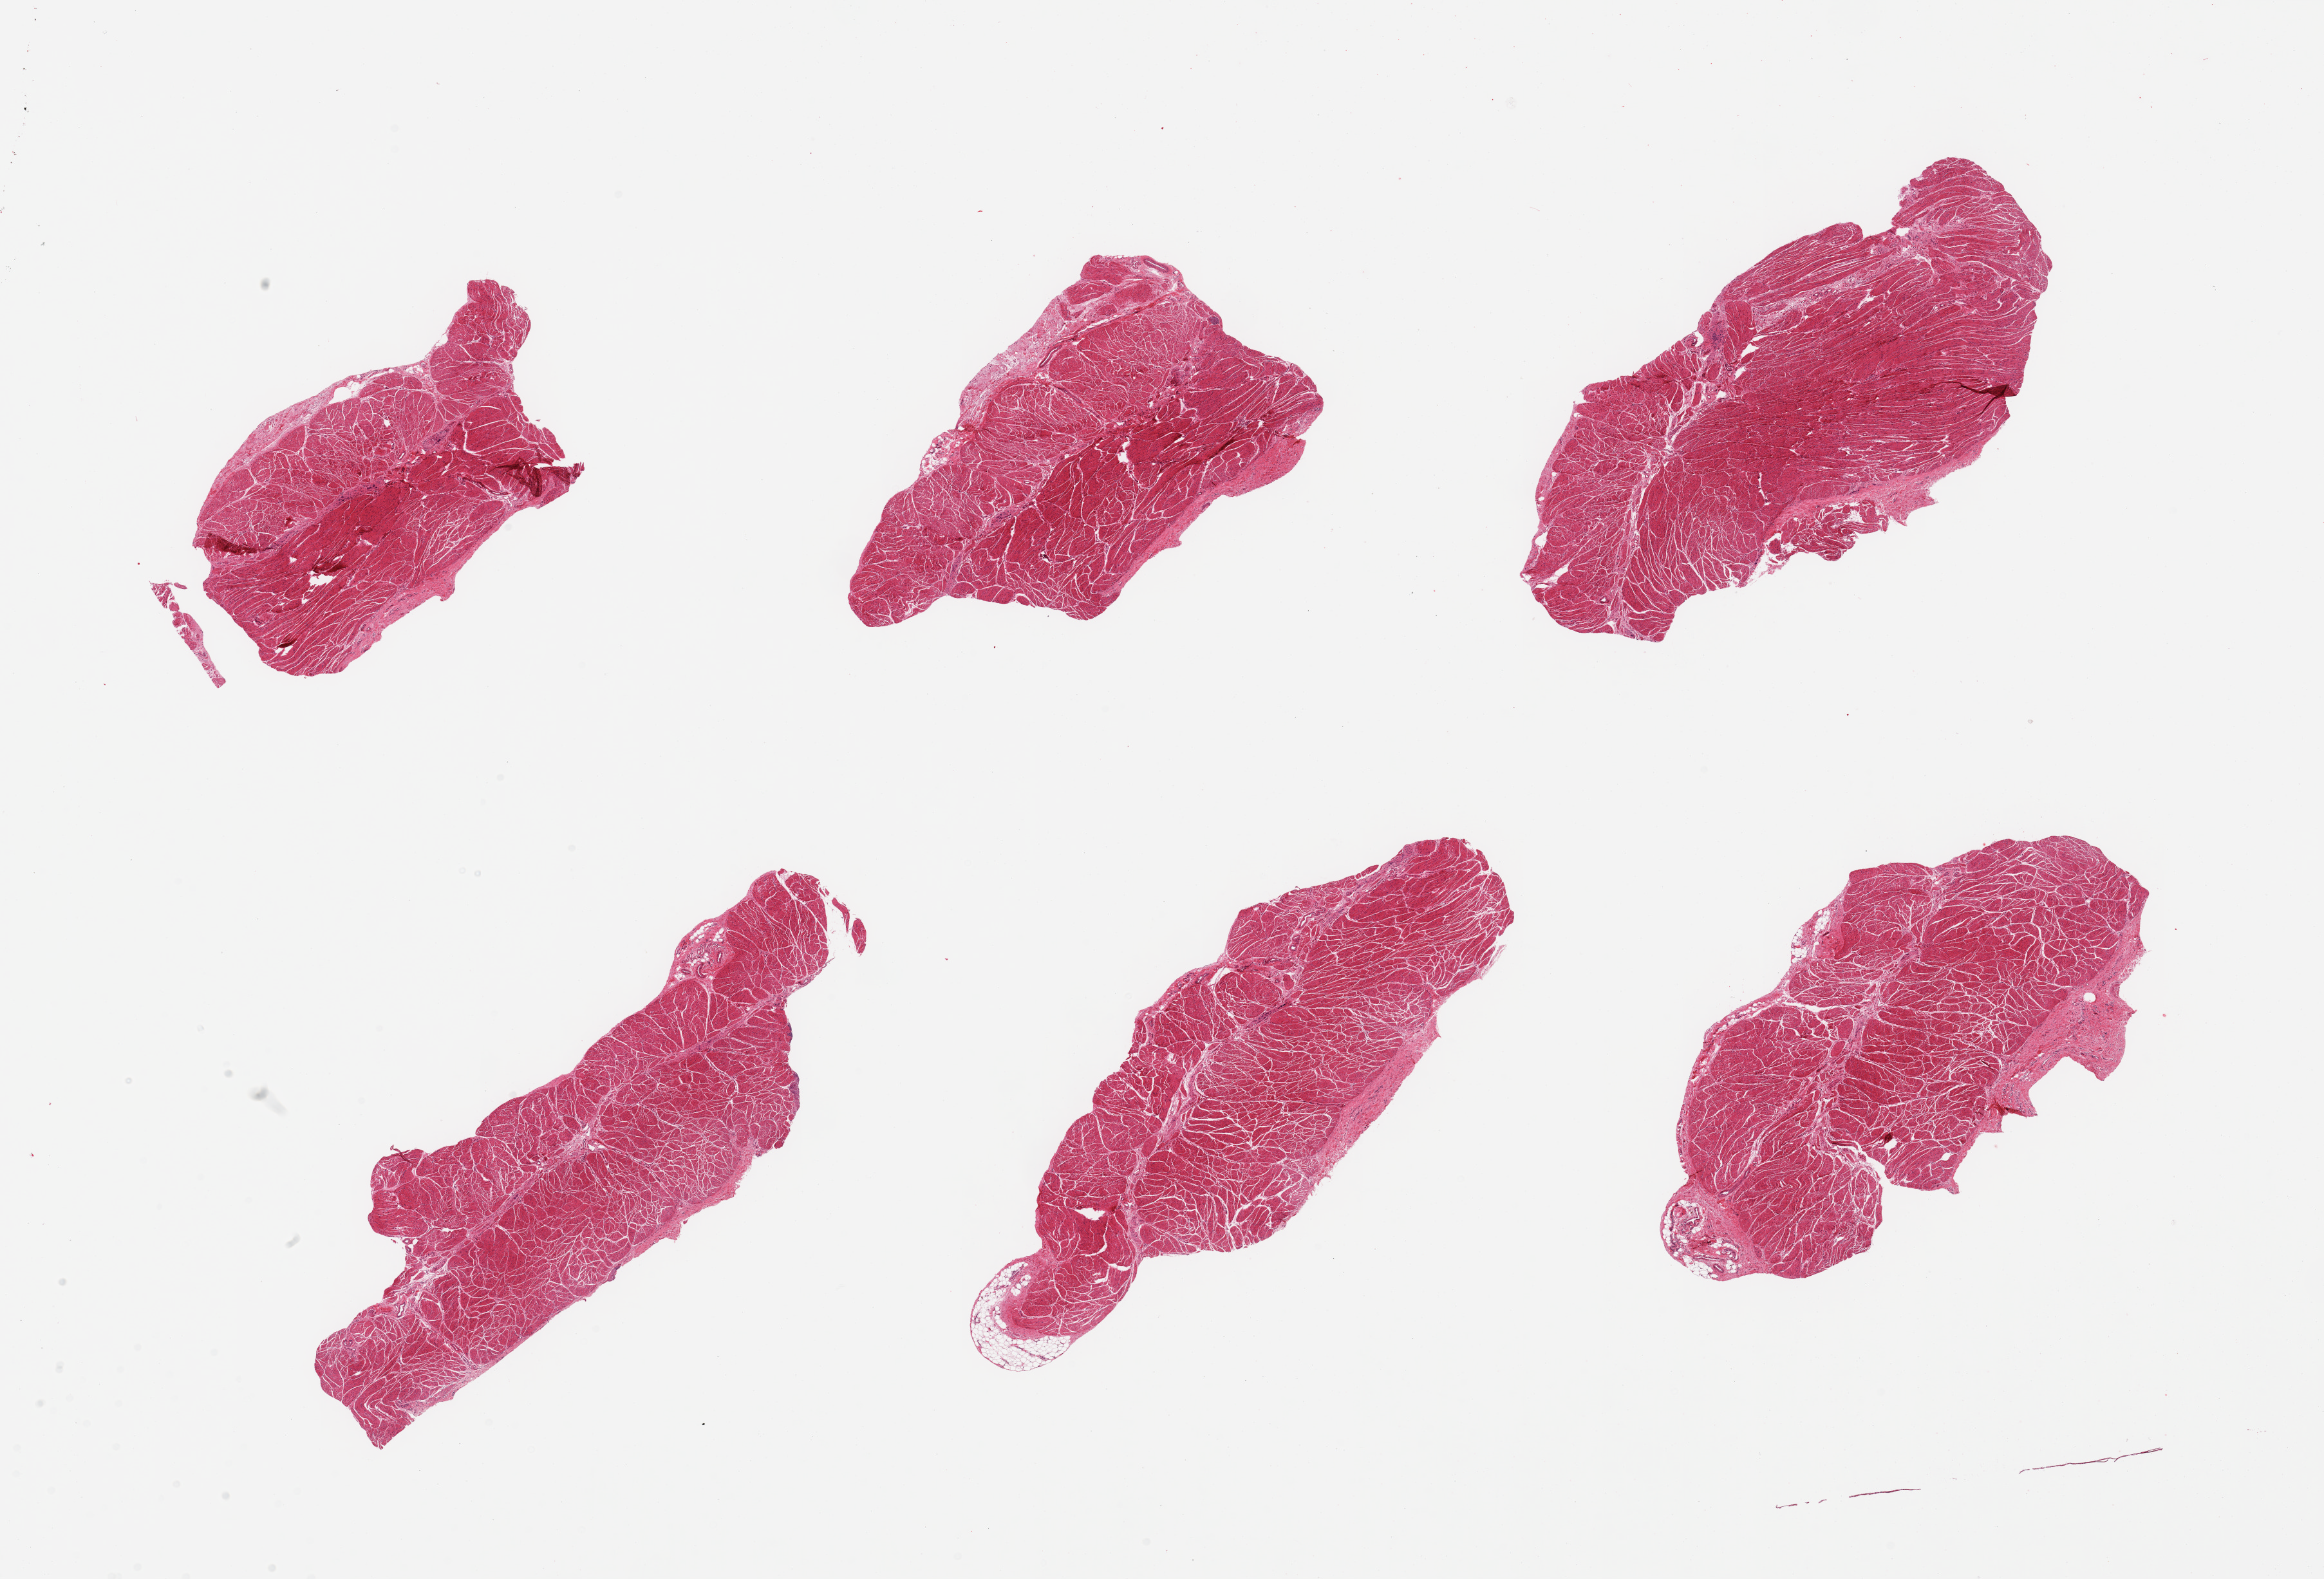
Digitized hematoxylin and eosin (H&E)-stained section — shown as a low-resolution overview of the whole scanned area (about 28.5 x 19.4 mm, from a 20x scan), PAXgene-fixed paraffin-embedded (PFPE) section, section of esophageal muscle (target tissue), tissue donor sample. Male donor.
* review note (as recorded): 6 pieces, confirmed target muscularis